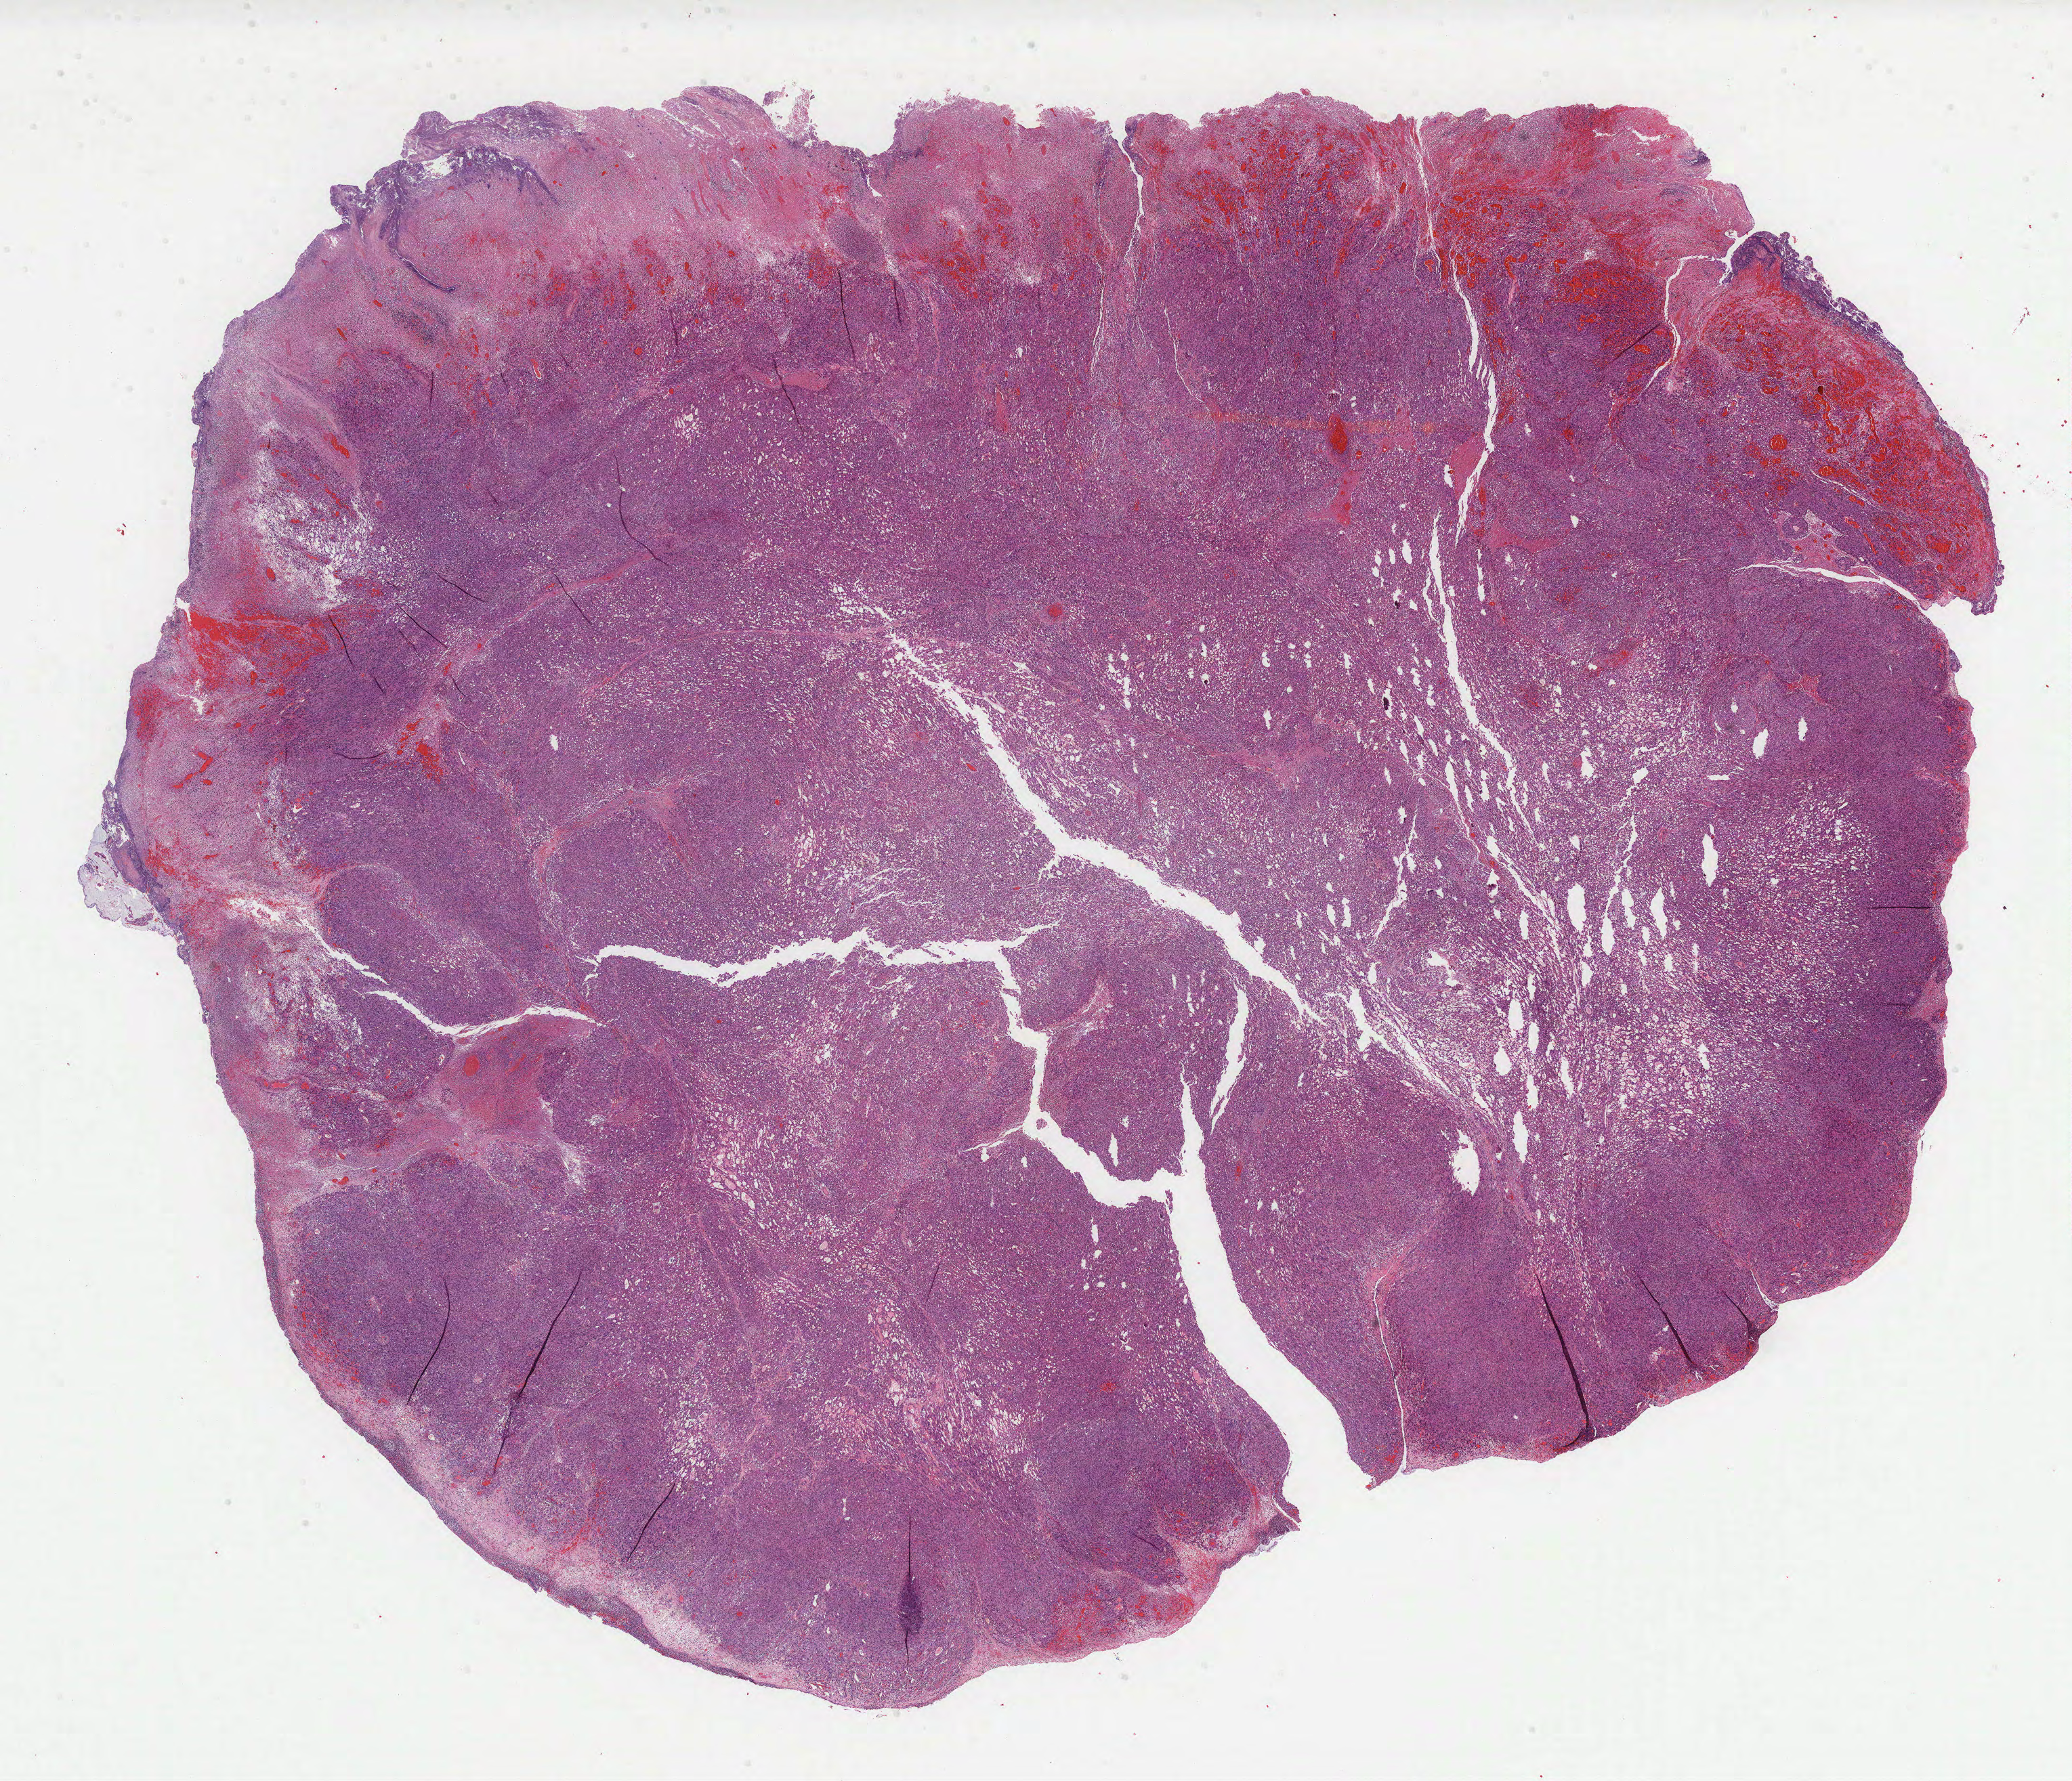
Hematoxylin and eosin (H&E) stained whole-slide image — low-resolution overview of the scanned area, about 24.7 x 21.2 mm (slide scanned at 40x). FFPE section. Retroperitoneum and peritoneum, primary tumour sample. Patient: female, age at initial diagnosis 70 years.
Histologic diagnosis: Leiomyosarcoma, NOS (retroperitoneum).